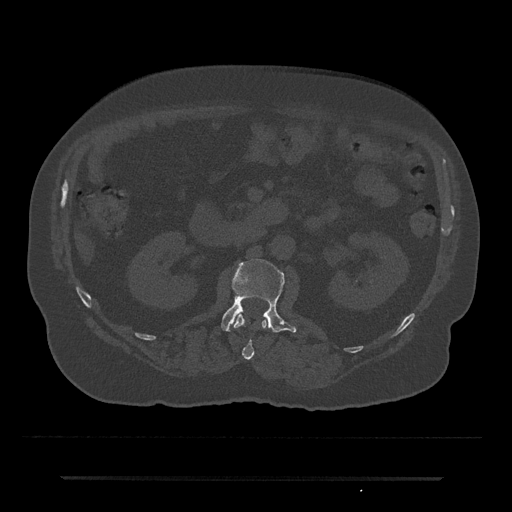
CT including the spine, one axial slice; slice 29 of 797 in the series (ordered by position); 120 kVp; bone window (W 1800 / L 400 HU); 512 × 512 image matrix, field of view 437 × 437 mm. Male patient, age 69 years. From the clinical record (not read from this slice): primary cancer: prostate.
Outlined on this slice (semi-automatic segmentation, software-assisted and operator-edited):
- L1 vertebra: box from (x=234, y=314) to (x=267, y=360) px
- L2 vertebra: (x=221, y=258)–(x=297, y=333)